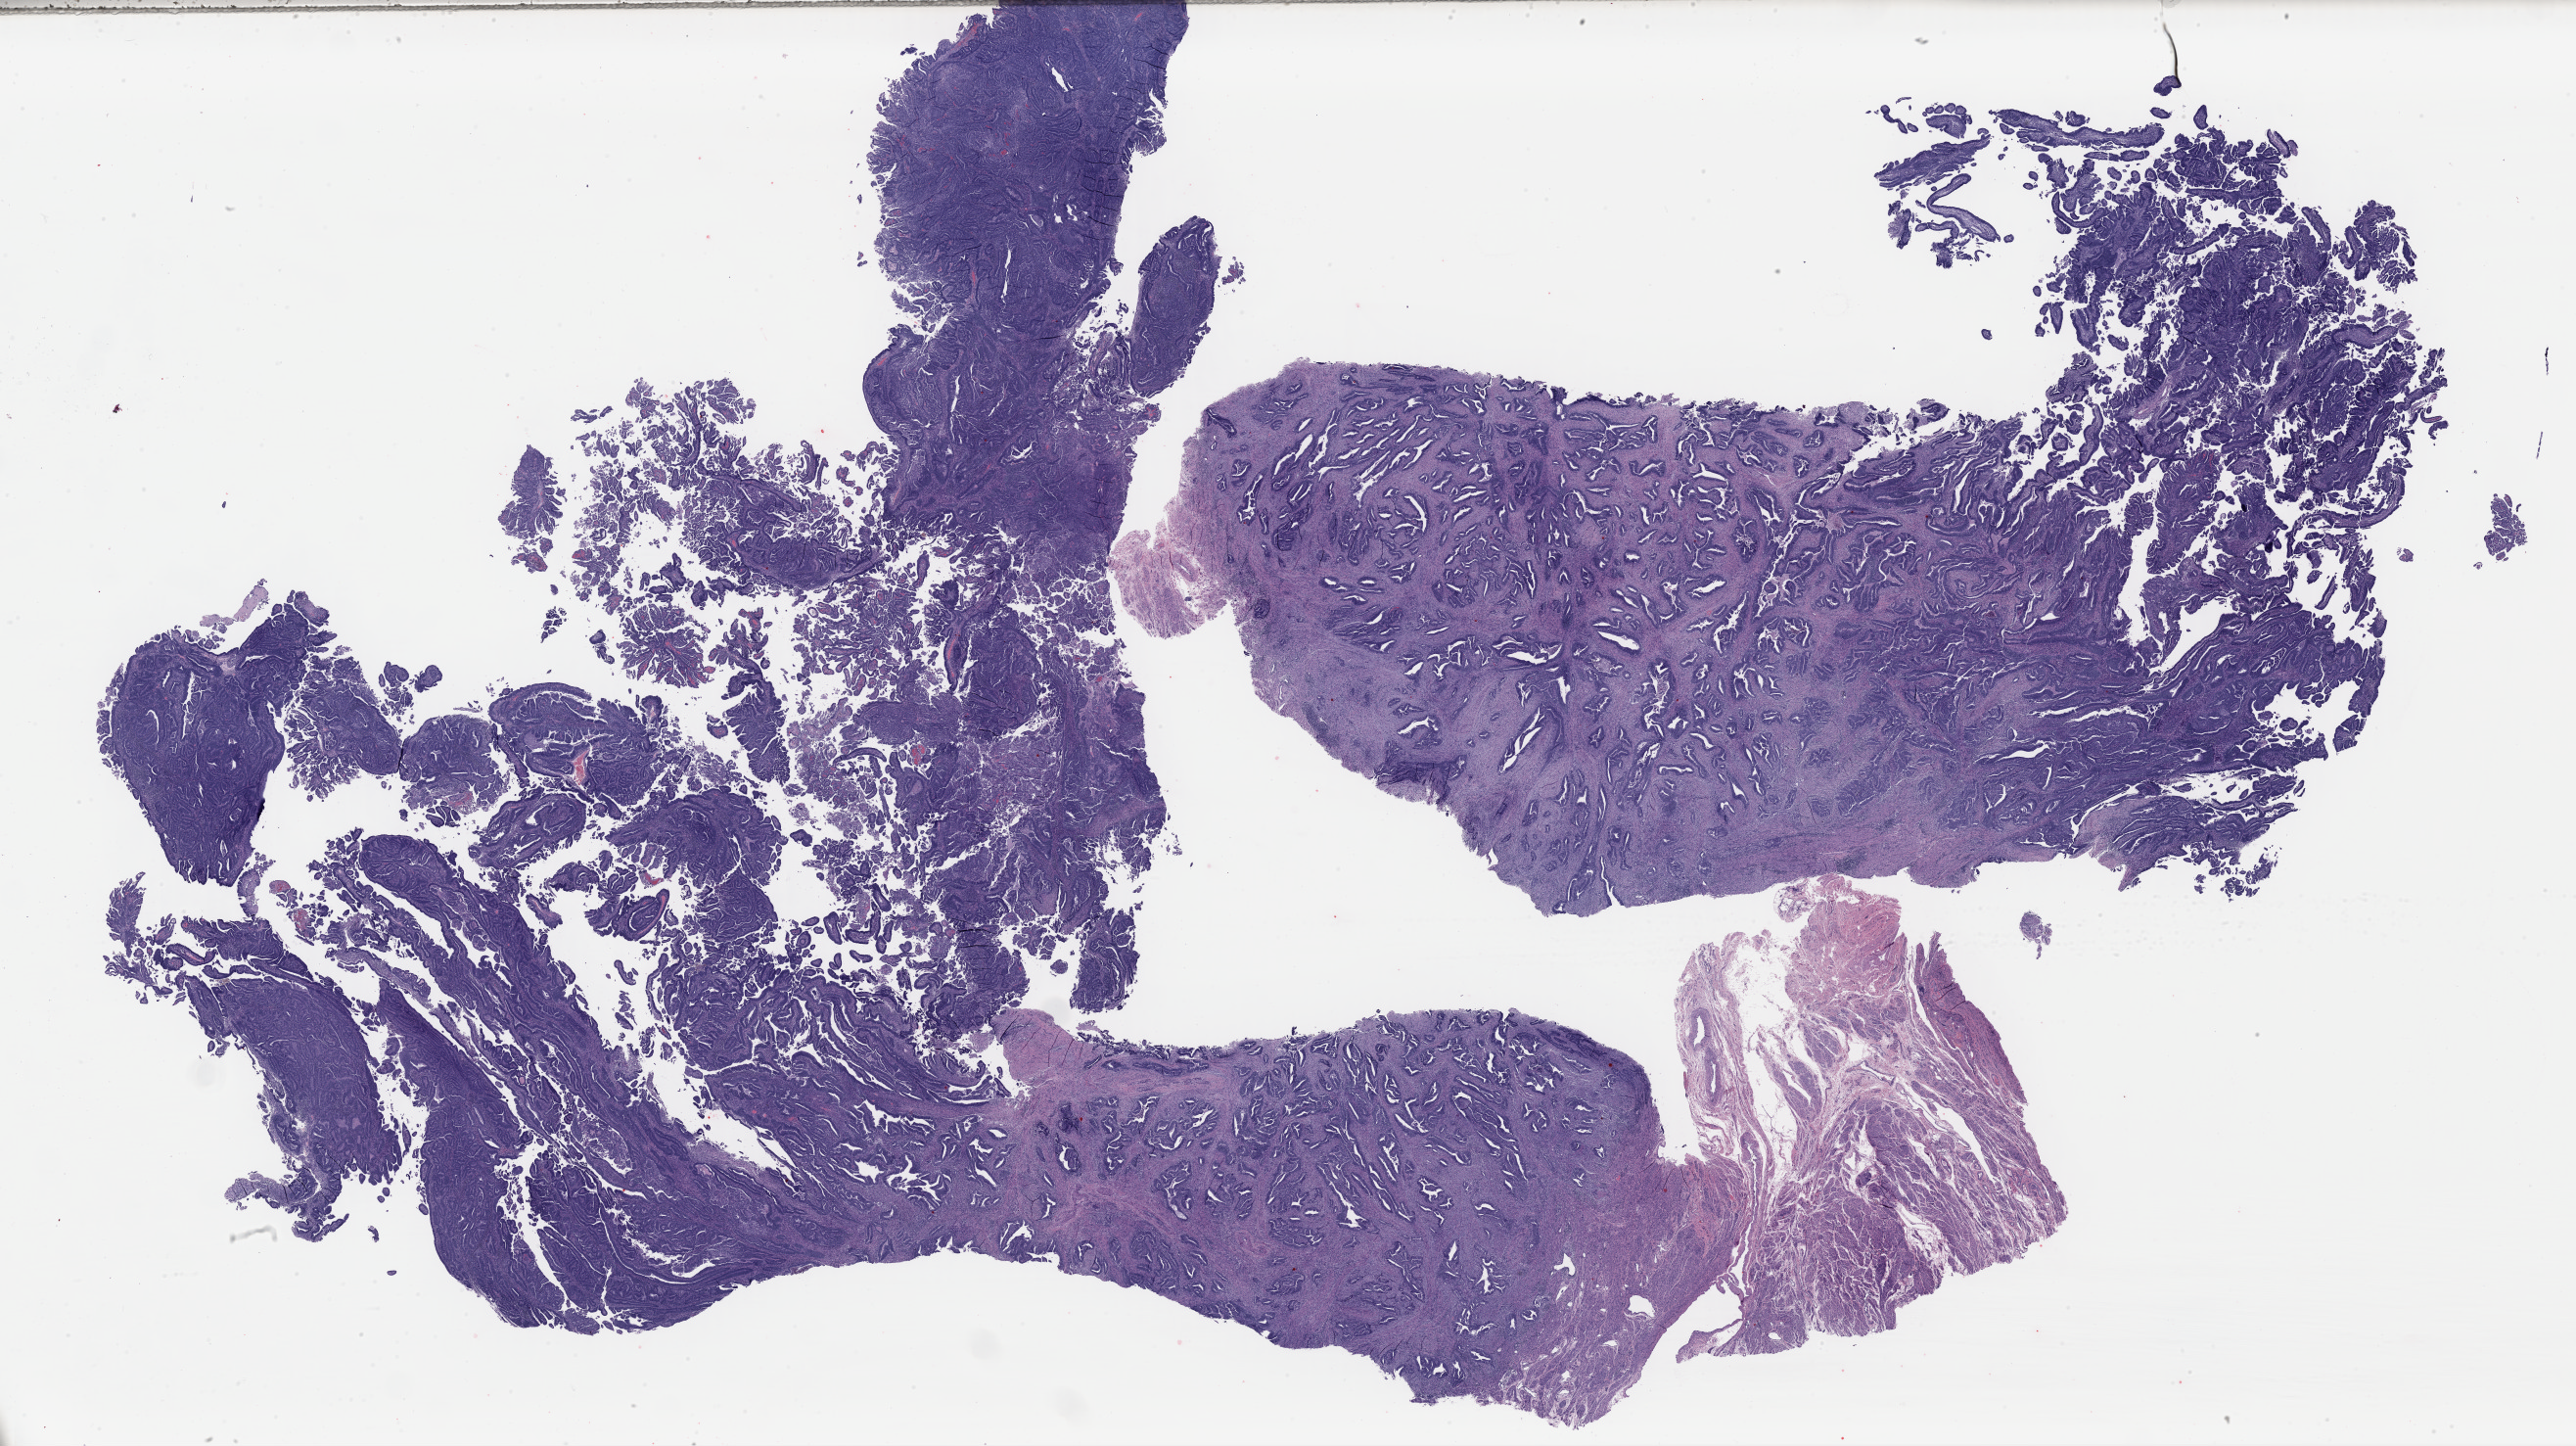
Whole-slide histology image, Hematoxylin and eosin (H&E) stained — whole scanned area (about 41.6 x 23.3 mm) shown as a low-resolution overview. Formalin-fixed paraffin-embedded (FFPE) diagnostic section. Sample: primary tumour, uterus. Female, age 57 years at initial diagnosis. Histologic grade: G3 (poorly differentiated).
Pathologic diagnosis: Serous cystadenocarcinoma, NOS (endometrium). FIGO stage: IB.